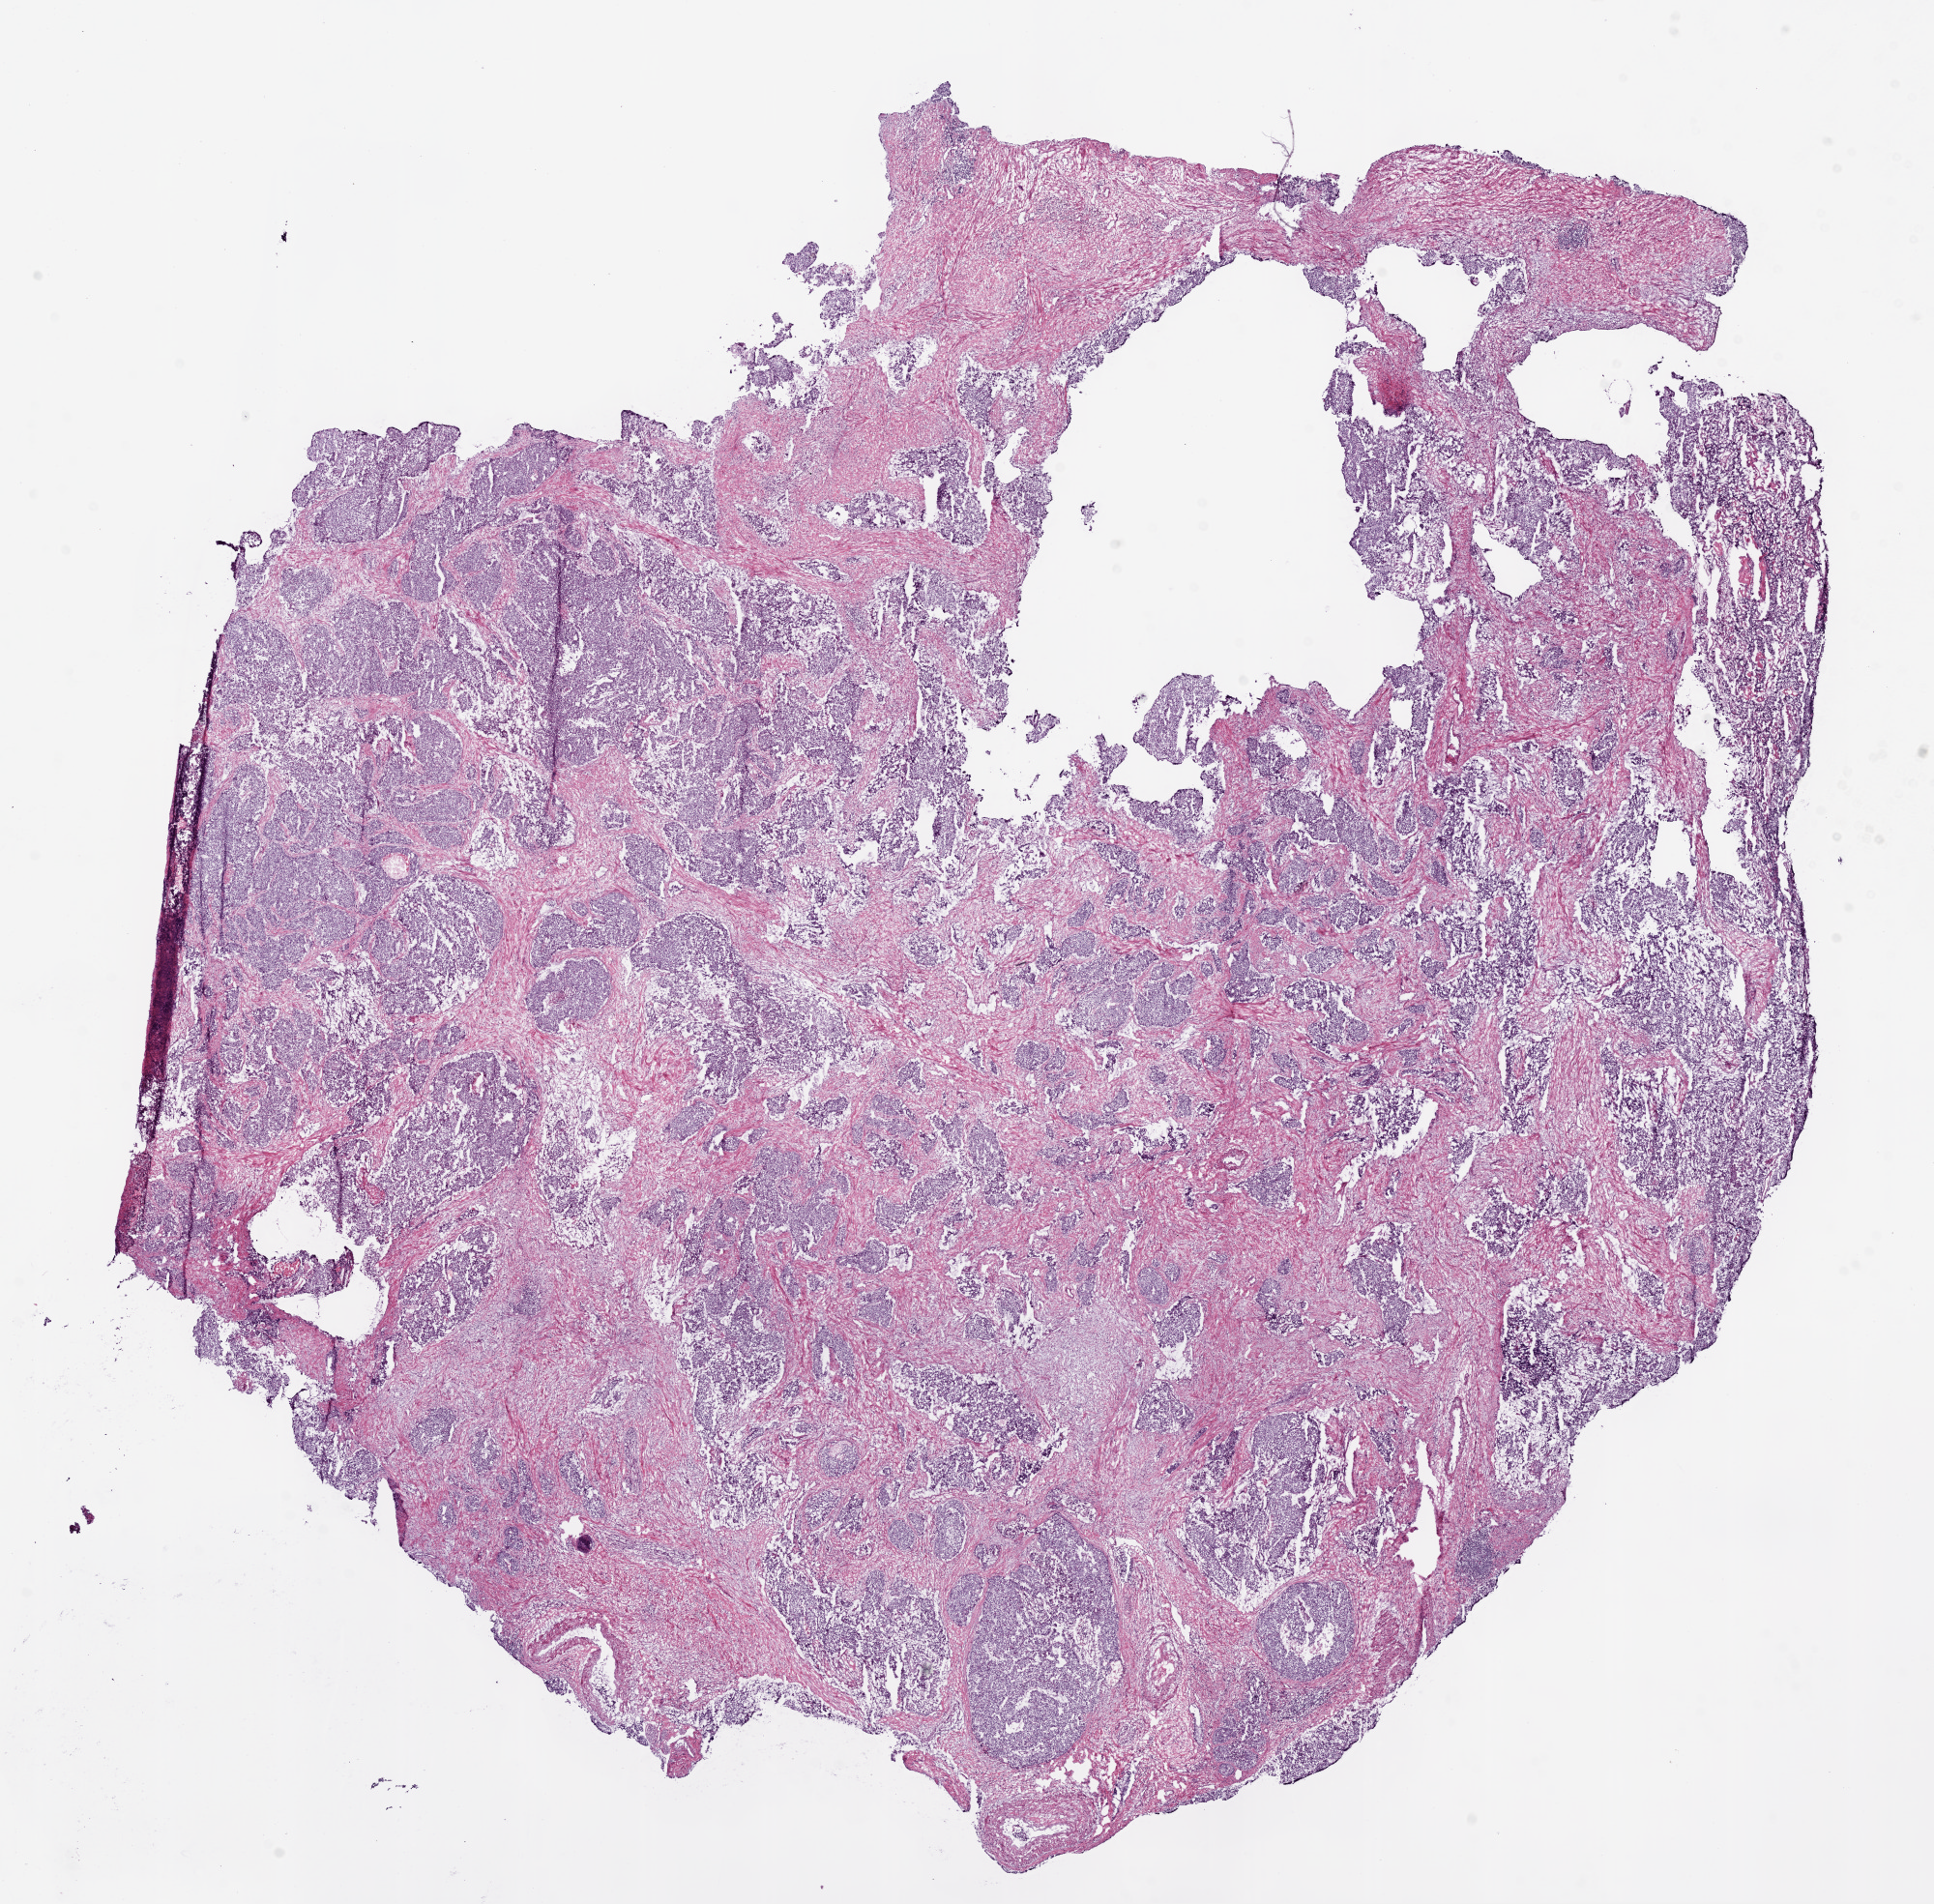
Whole-slide histology image, H&E-stained, whole scanned area (about 16.0 x 15.8 mm, acquisition: 20x scan) shown as a low-resolution overview; frozen section from the top of the tissue portion; sample: primary tumour, prostate. Male, age 67 years at initial diagnosis. Gleason score: 9 (4+5). Pathologist review of this section (percent, as recorded): tumour cells 55%, tumour nuclei 60%, normal cells 10%, stromal cells 30%, necrosis 5%. Inflammatory infiltration, as recorded: lymphocyte infiltration 5%, monocyte infiltration 5%, neutrophil infiltration 0%.
Diagnosis: Acinar cell carcinoma (prostate gland).